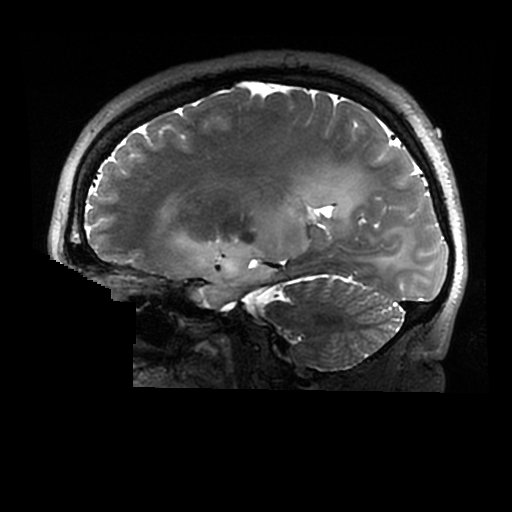
Brain MRI from a brain-tumour surgery series, one sagittal slice; position 182 of 320 along the scan axis; 0.6 mm slice thickness; 512 × 512 image matrix, field of view 240 × 240 mm. Case-level facts recorded for this patient, not image findings: histopathology: Astrocytoma; WHO grade: 2; IDH mutation: yes.
Structures marked on this image (outlined manually by an expert reader):
- tumour: box from (x=177, y=186) to (x=388, y=309) px